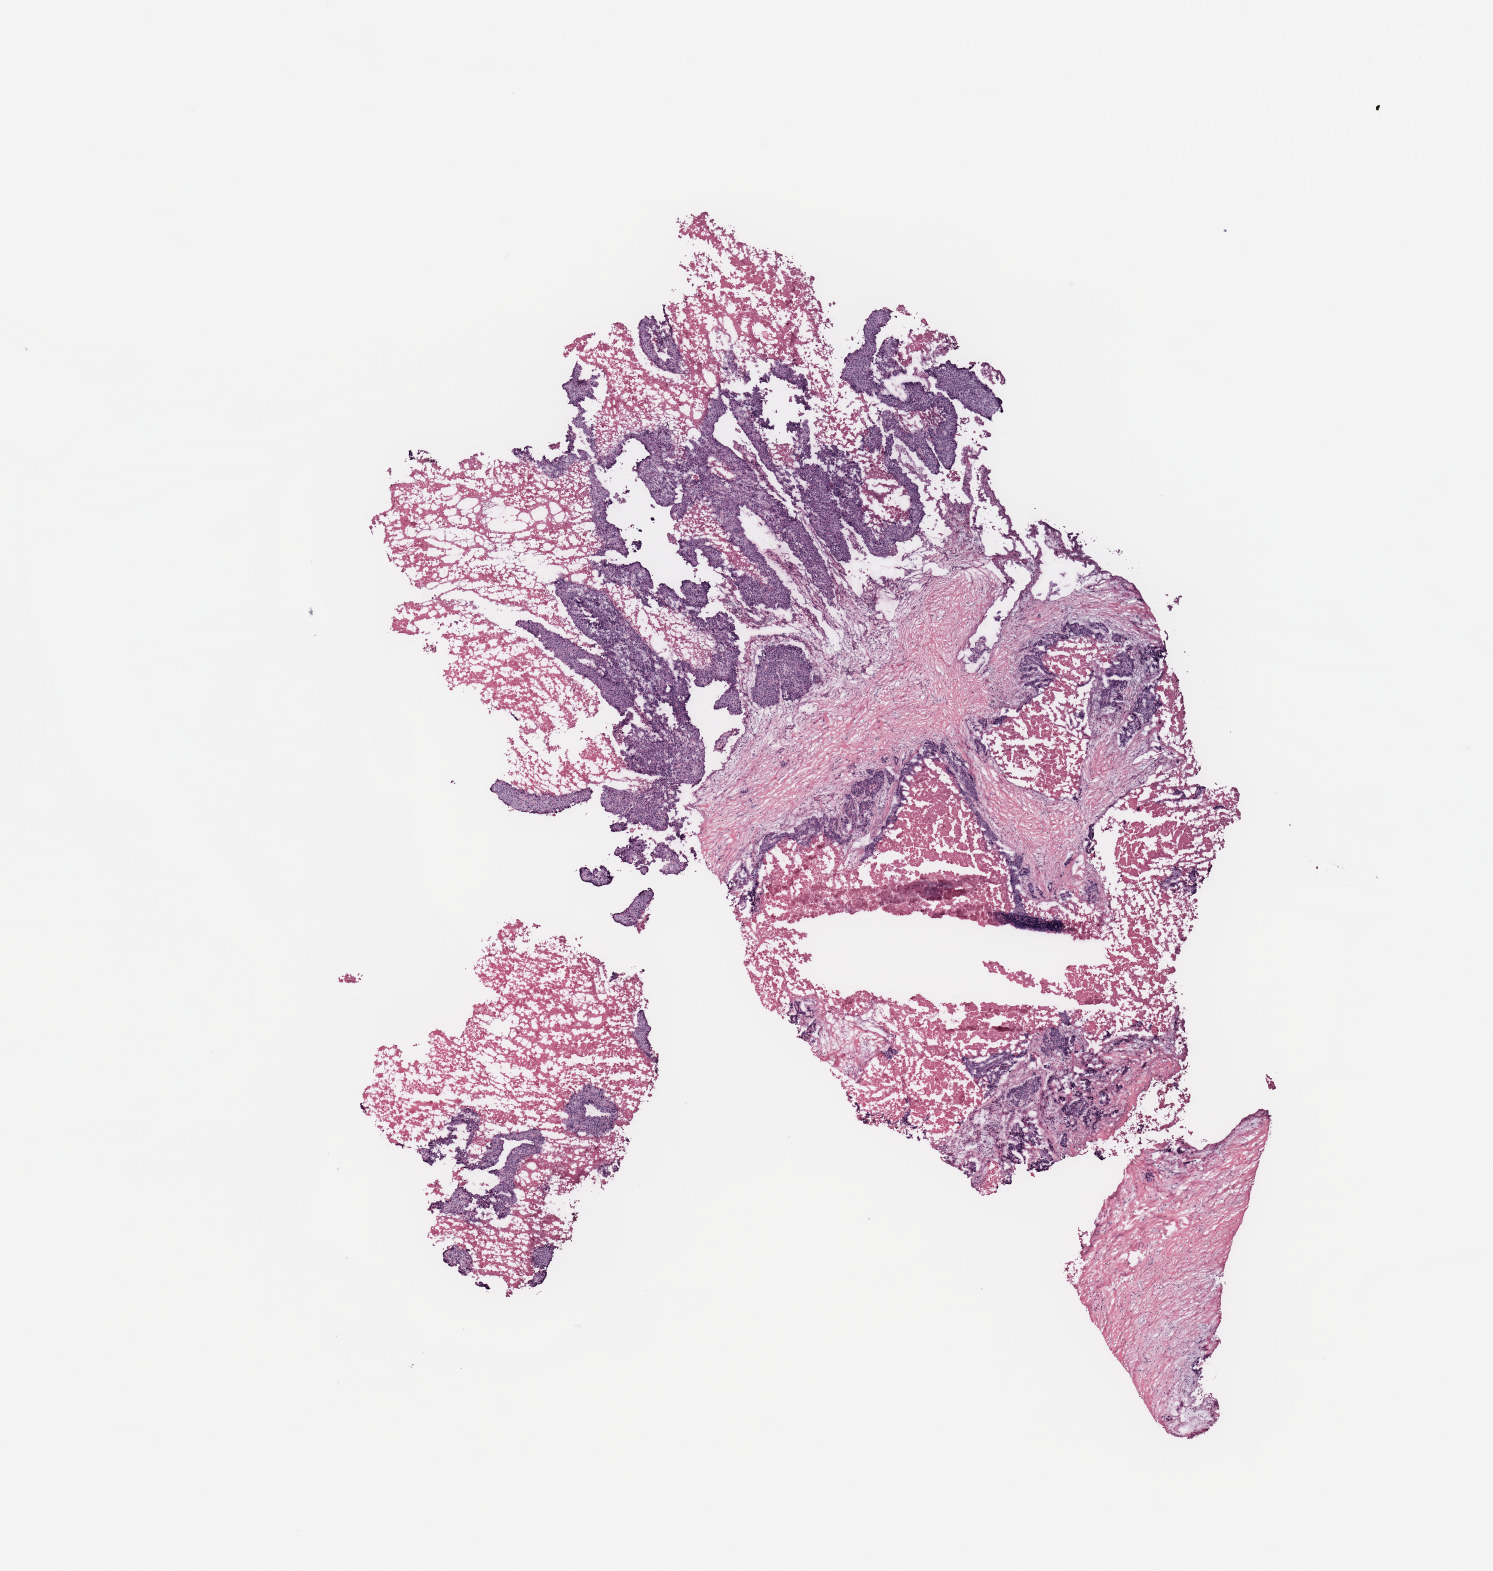
Digitized Hematoxylin and eosin (H&E) stained tissue section (whole slide) — a low-resolution overview of the entire scanned area, about 11.8 x 12.4 mm (from a 20x scan). Breast, tissue type not recorded.
Patient diagnosis (cohort enrolment): breast cancer (breast).